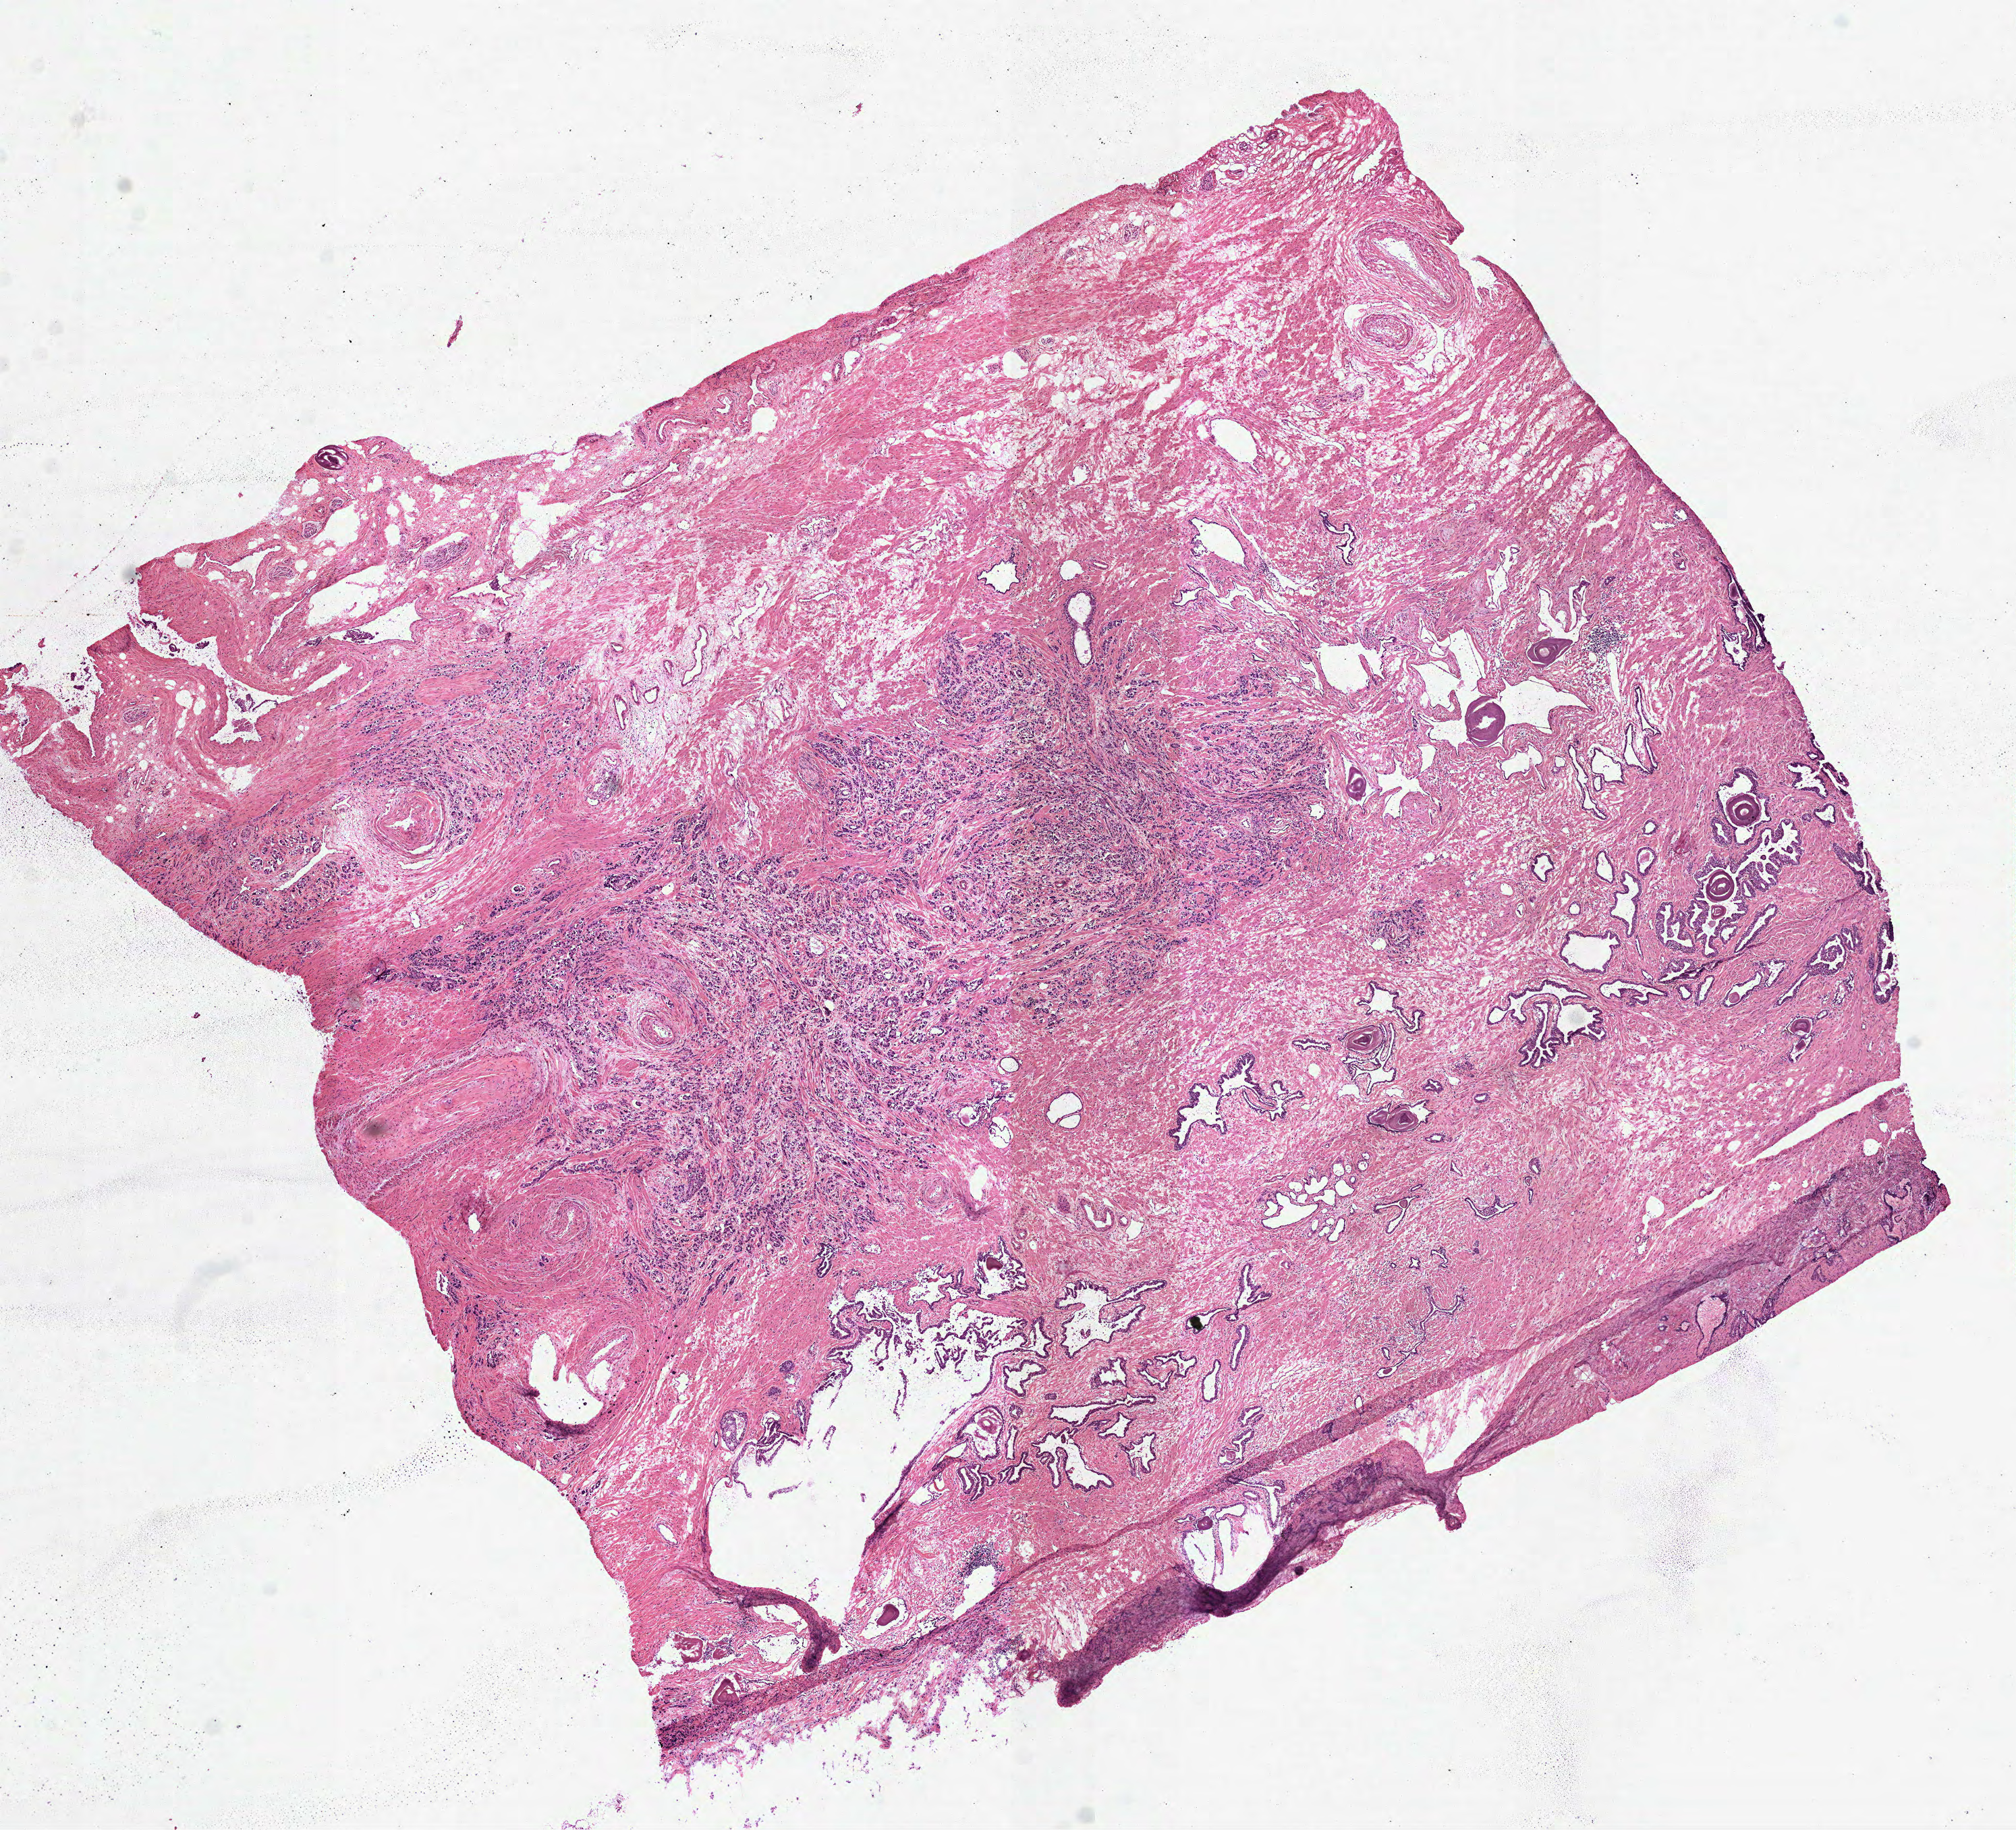
Whole-slide histology image, Hematoxylin and eosin (H&E) stained — a low-resolution overview of the entire scanned area, about 12.0 x 10.9 mm (slide scanned at 40x). Frozen section from the top of the tissue portion. Sample: primary tumour, prostate. Patient: male, age at initial diagnosis 66 years. Gleason score: 9 (4+5). Composition of this section per pathologist review: tumour cells 60%, tumour nuclei 60%, normal cells 15%, stromal cells 25%, necrosis 0%. Inflammatory infiltration, as recorded: lymphocyte infiltration 3%, monocyte infiltration 0%, neutrophil infiltration 0%.
Lymph nodes positive (case pathology): 0 of 13 examined. Diagnosis: Acinar cell carcinoma.